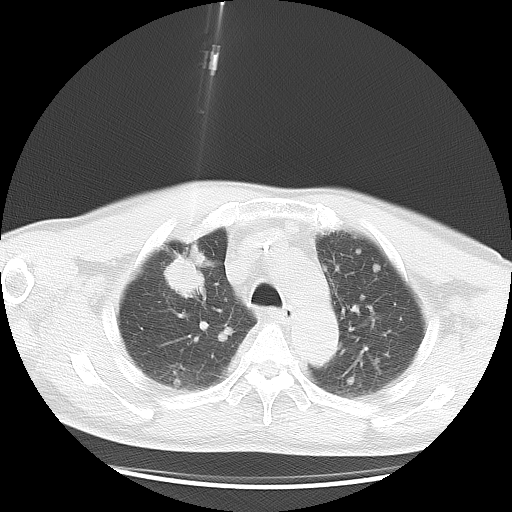
Chest CT, one axial slice; slice 22 of 35 in the series (ordered by position); reconstruction kernel LUNG; 120 kVp; lung window (W 1500 / L -600 HU); 5 mm slice thickness; 512 × 512 image matrix. Patient: male, 57 years. Case-level facts recorded for this patient, not image findings: clinical TNM (as recorded): T2 N3 M1a.
Annotated regions visible in this slice (rectangle marked by the reading radiologist):
- lung tumour (recorded histology: adenocarcinoma): bounding box <163,248,213,304> (left, top, right, bottom; pixels)